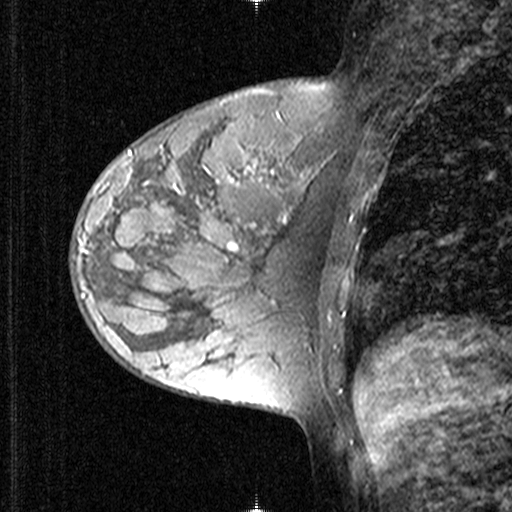
Breast MRI (dynamic contrast-enhanced), one sagittal slice; position 16 of 44 along the scan axis; dynamic contrast-enhanced study with each time point stored as its own series, time point 2 of 3 at this slice position (early post-contrast, ordered by acquisition time); 1.5 T; TE 4.5 ms, TR 11 ms; 3 mm slice thickness; 512 × 512 image matrix. Patient: female, 27 years. From the clinical record (not read from this slice): setting: breast cancer imaged before/during neoadjuvant chemotherapy; receptor status: HR-positive, HER2-negative.
Outlined on this slice (semi-automatically segmented with operator editing):
- analysis volume of interest (the breast-tissue region the enhancement analysis was run in; not a lesion): bounding box (x1, y1, x2, y2) in pixels: (72, 146, 165, 239)
- tumour enhancement mask (voxels above the 90 % enhancement threshold inside the analysis volume of interest): (130, 150, 133, 155)